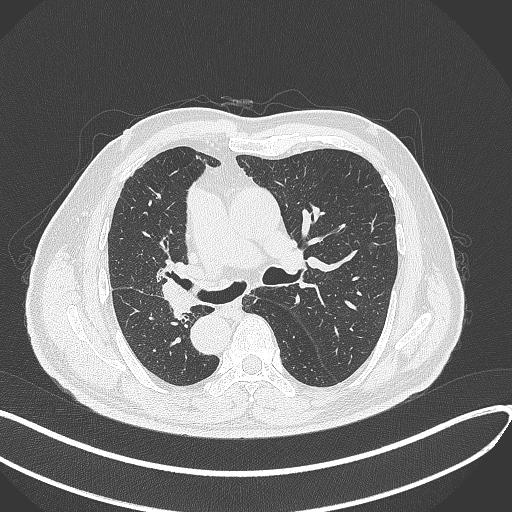
Chest CT, one axial slice; slice 173 of 300 in the series (ordered by position); lung window (W 1500 / L -600 HU); 1 mm slice thickness; 512 × 512 image matrix. Patient: male, 67 years. Case-level facts recorded for this patient, not image findings: clinical TNM (as recorded): T2a N0 M0.
Outlined on this slice (bounding box drawn by a radiologist):
- lung tumour (recorded histology: squamous cell carcinoma): bounding box [x1, y1, x2, y2] px = [158, 272, 201, 322]